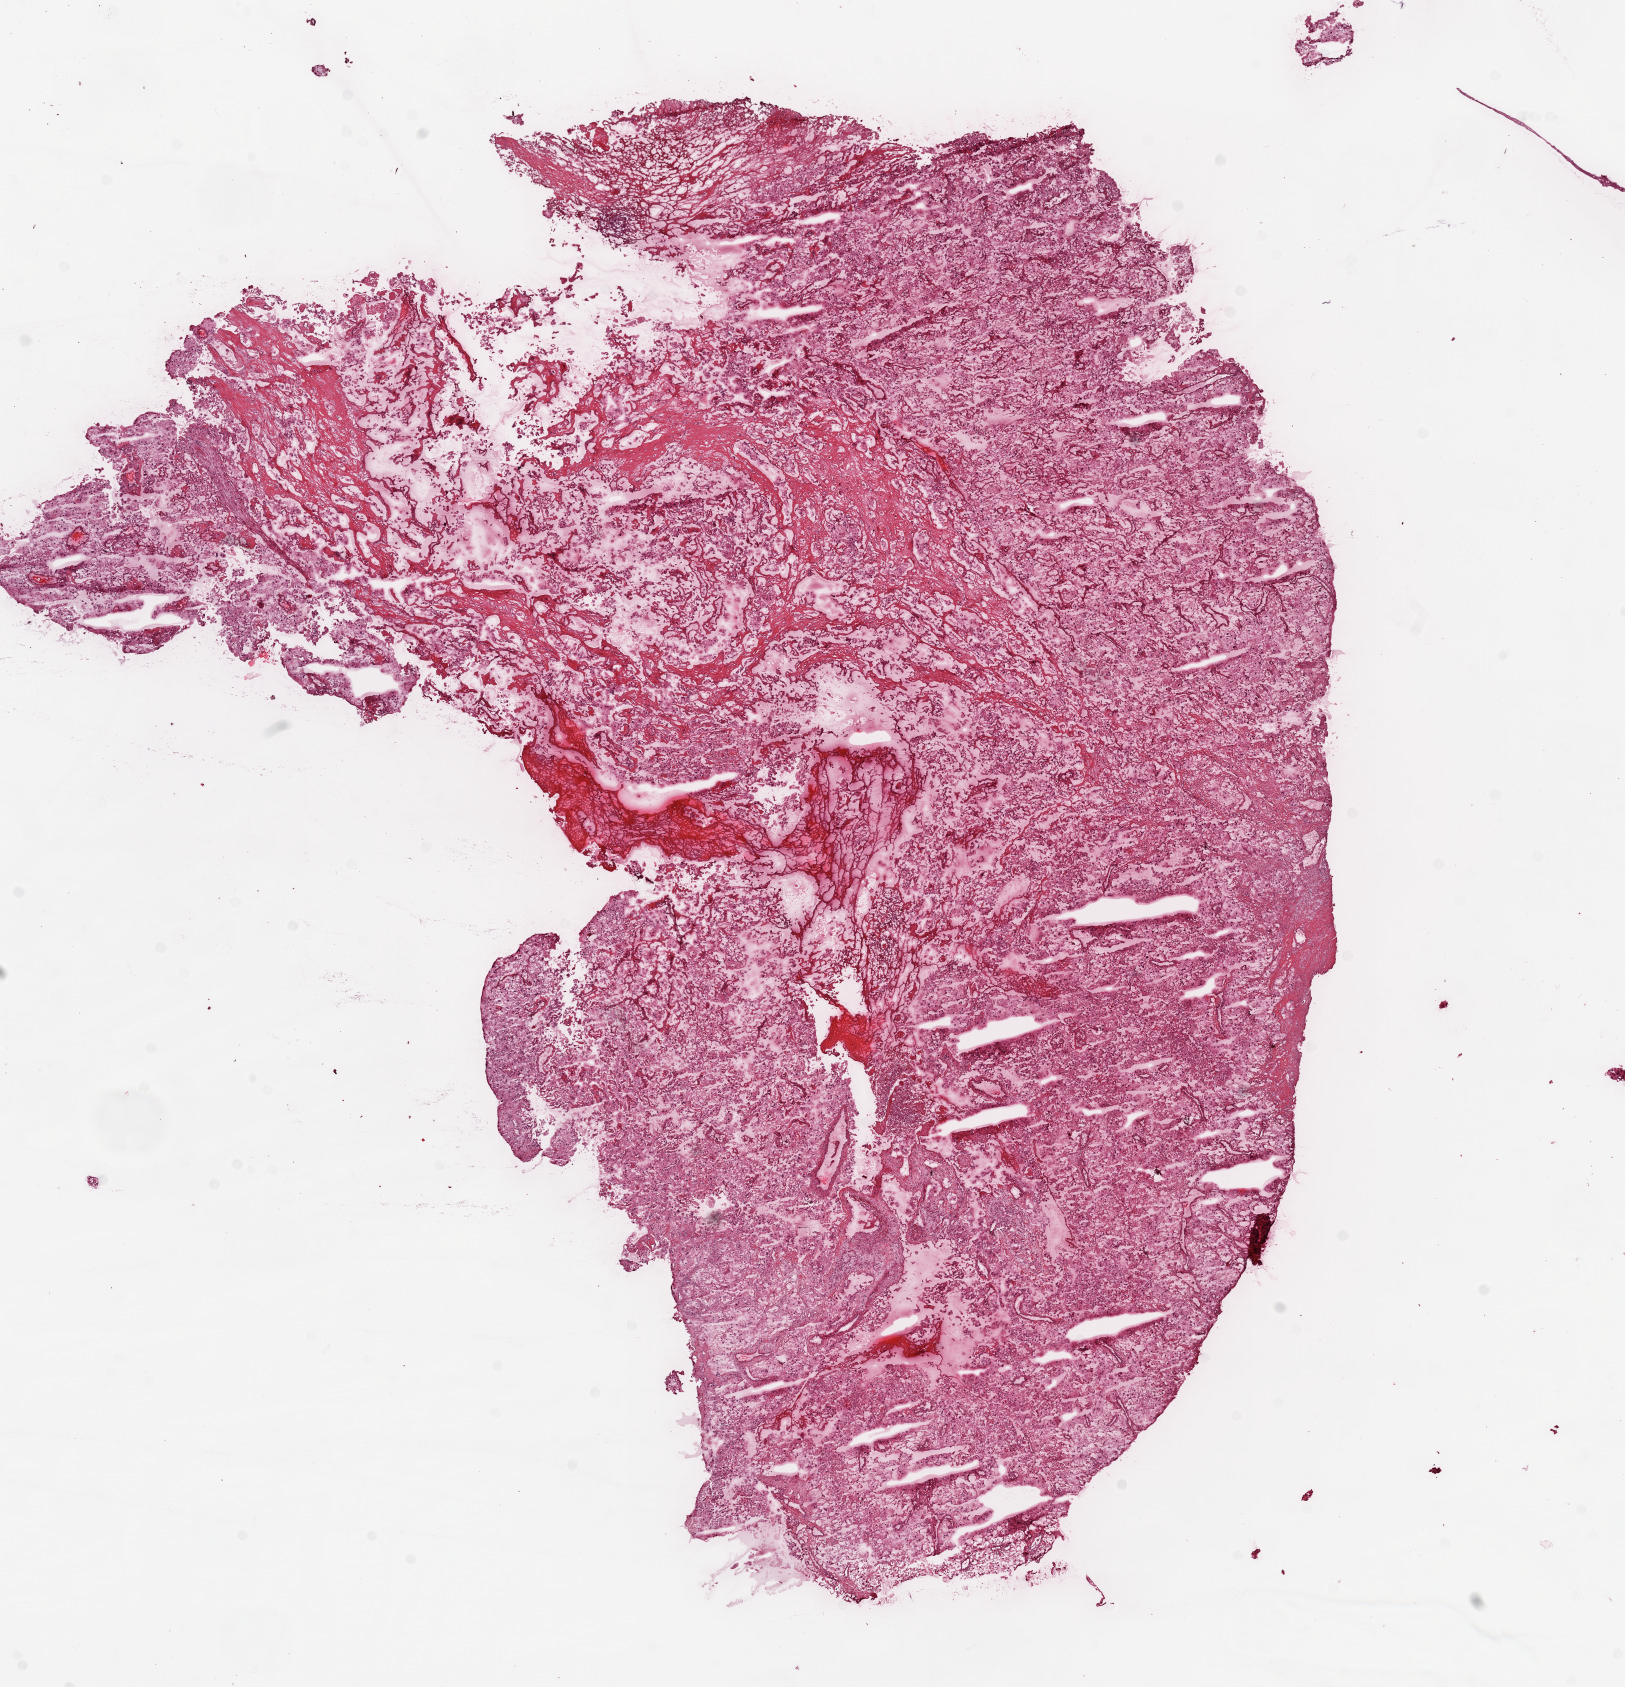
H&E-stained whole-slide image — whole scanned area (about 13.0 x 13.5 mm) shown as a low-resolution overview. Frozen section. Sample: primary tumour, kidney. Patient: male, age at initial diagnosis 72 years.
Histologic diagnosis: Clear cell adenocarcinoma, NOS.